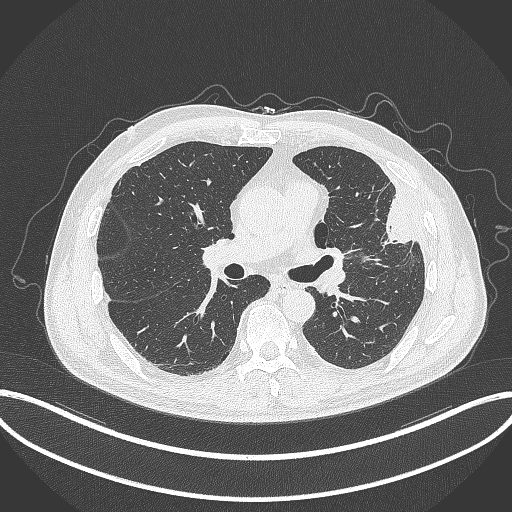
Chest CT, one axial slice. Slice 187 of 382 in the series (ordered by position). 120 kVp. Lung window (W 1500 / L -600 HU). 1 mm slice thickness. 512 × 512 image matrix, field of view 415 × 415 mm. Male patient, age 64 years. From the clinical record (not read from this slice): clinical TNM (as recorded): T4 N1 M0; histopathological grade: G3.
Structures marked on this image (rectangle marked by the reading radiologist):
- lung tumour (recorded histology: adenocarcinoma): bounding box (x1, y1, x2, y2) in pixels: (375, 195, 424, 246)